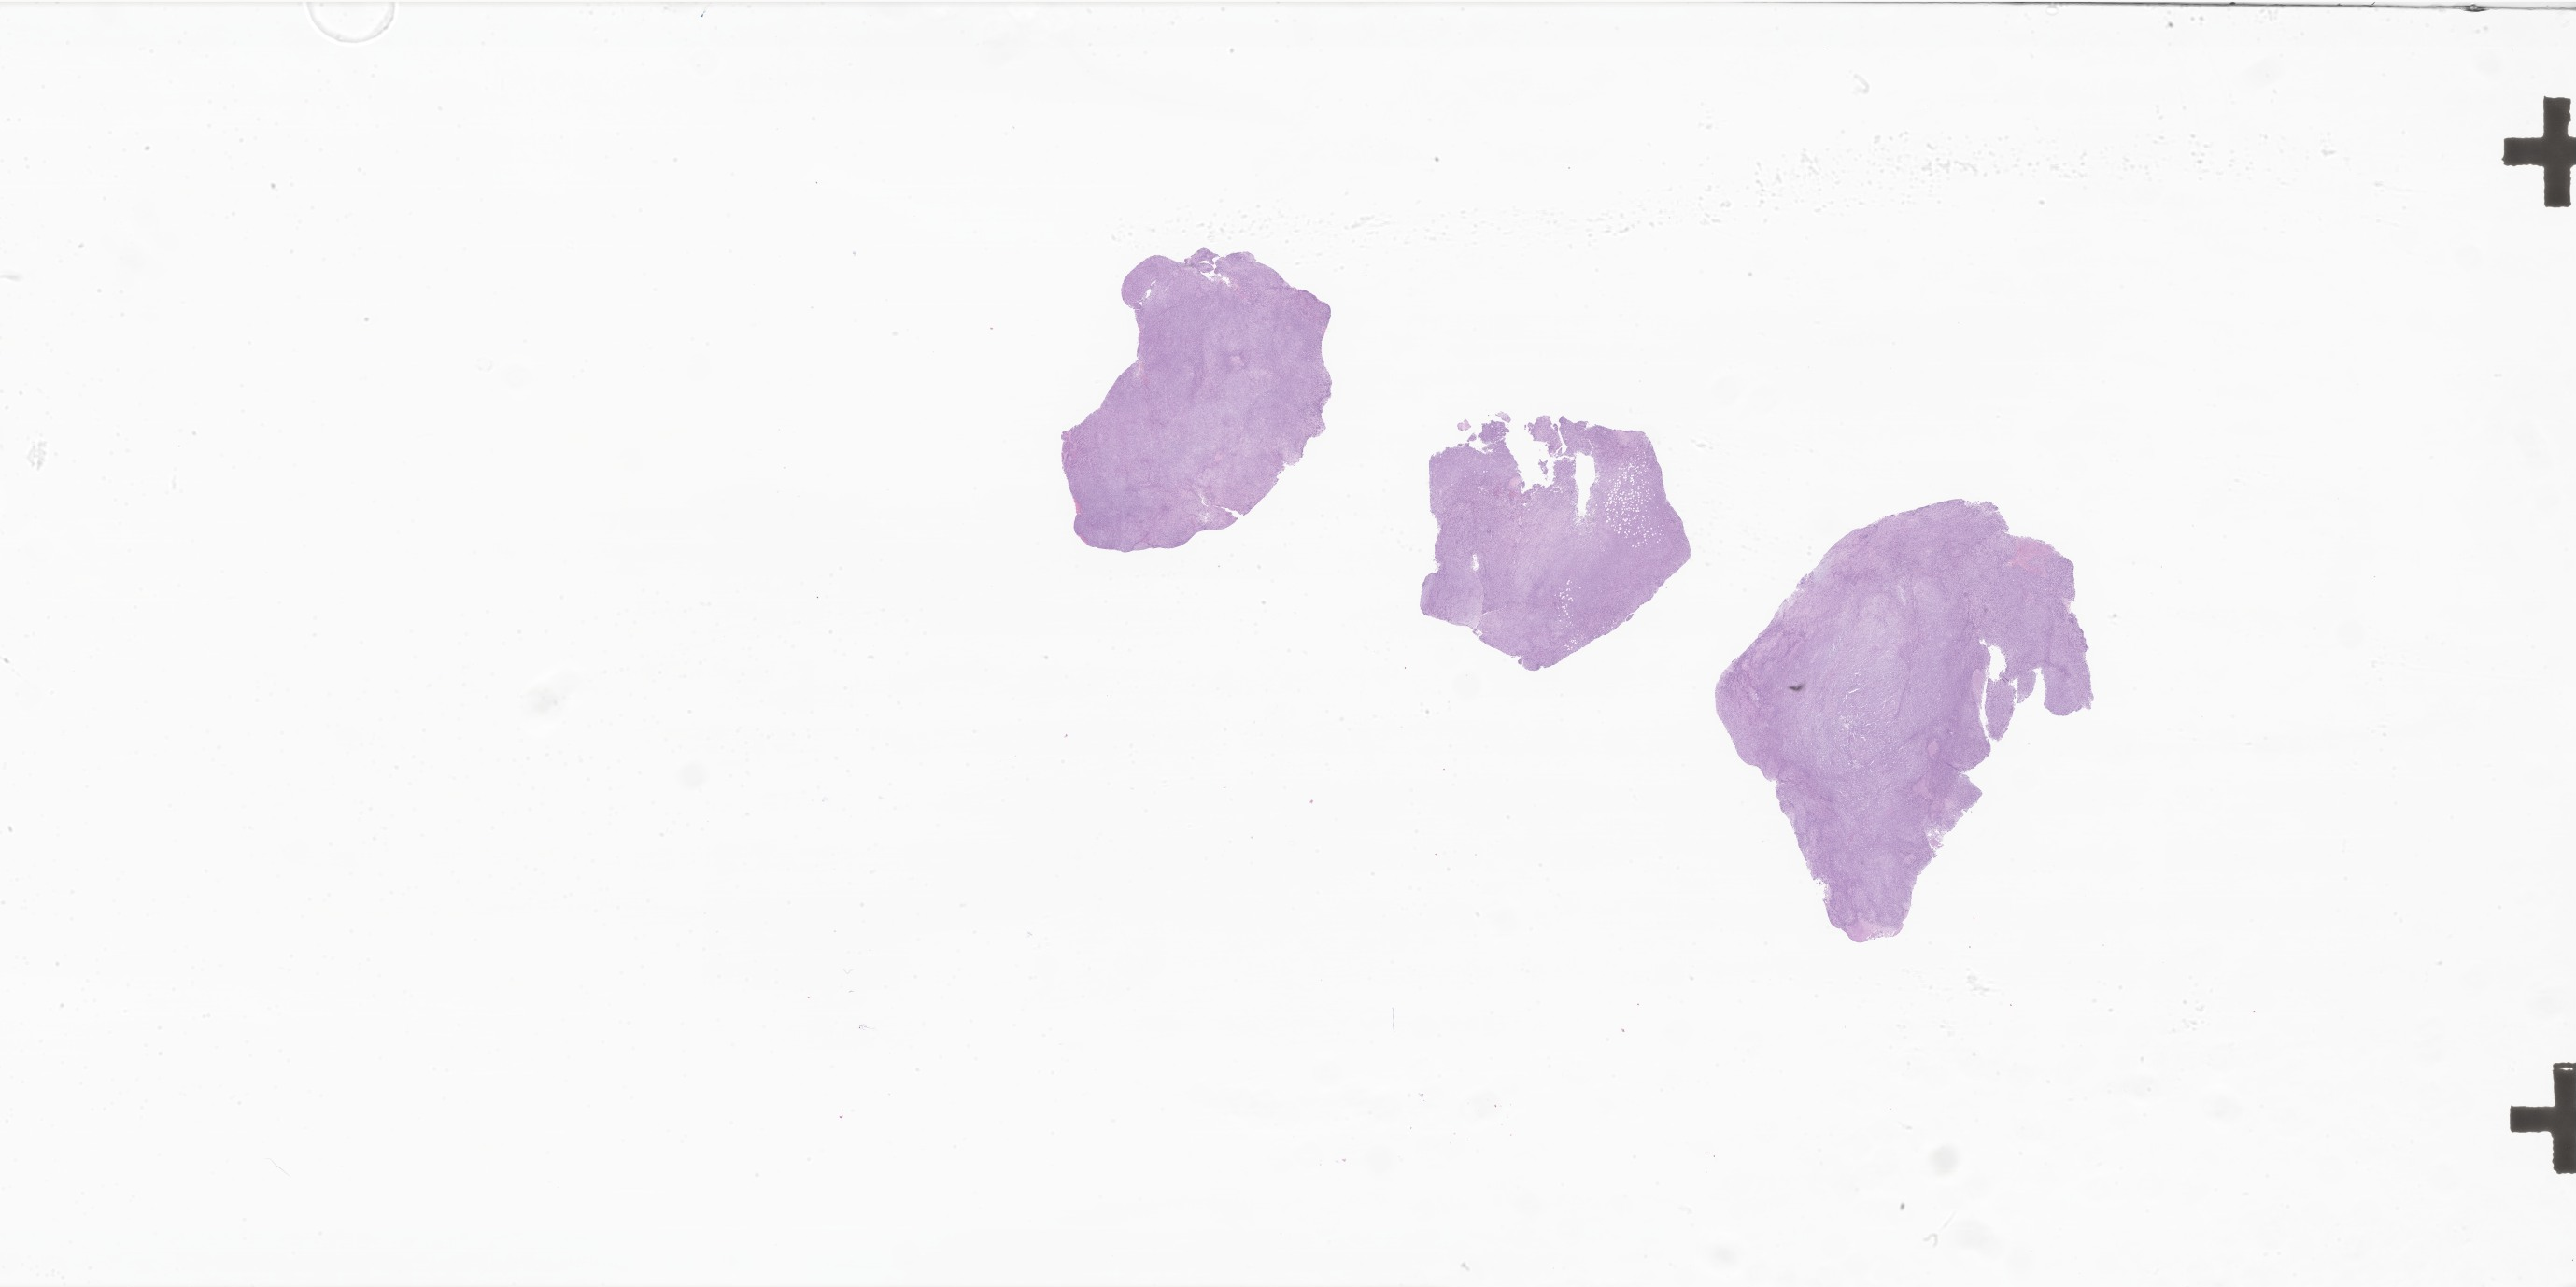
Whole-slide image, hematoxylin and eosin (H&E) stain of tumor tissue from the posterior mediastinum — shown as a low-resolution overview of the whole scanned area (about 46.5 x 23.2 mm), FFPE section. Patient male; age 74 days.
- recorded diagnosis: Rhabdoid tumor, NOS